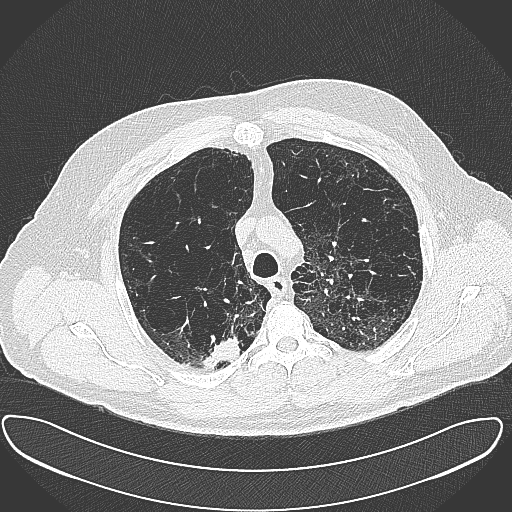
Axial slice from a low-dose chest CT screening exam. First (baseline) screen. Lung window (W 1500 / L -600 HU). 120 kVp. Slice 88 of 385 in the series. 512 × 512 image matrix. Male participant, aged 60 years at enrolment. Current smoker at enrolment.
• Expert-annotated lung lesion, bounding box (x1, y1, x2, y2) in pixels: (196, 327, 246, 371).
• Reader record for this screening exam (exam-level; its link to the box is not recorded): non-calcified nodule or mass ≥4 mm, right upper lobe, 15 × 25 mm, spiculated (stellate) margins, soft tissue attenuation.
• Official screen result: positive, change unspecified: nodule(s) >= 4 mm or enlarging nodule(s), mass(es), or other non-specific abnormalities suspicious for lung cancer.
• Lung cancer was diagnosed 32 days after this screen: carcinoma, NOS, right upper lobe, moderately differentiated (G2), stage IB (AJCC 6th edition), 35 mm at pathology.